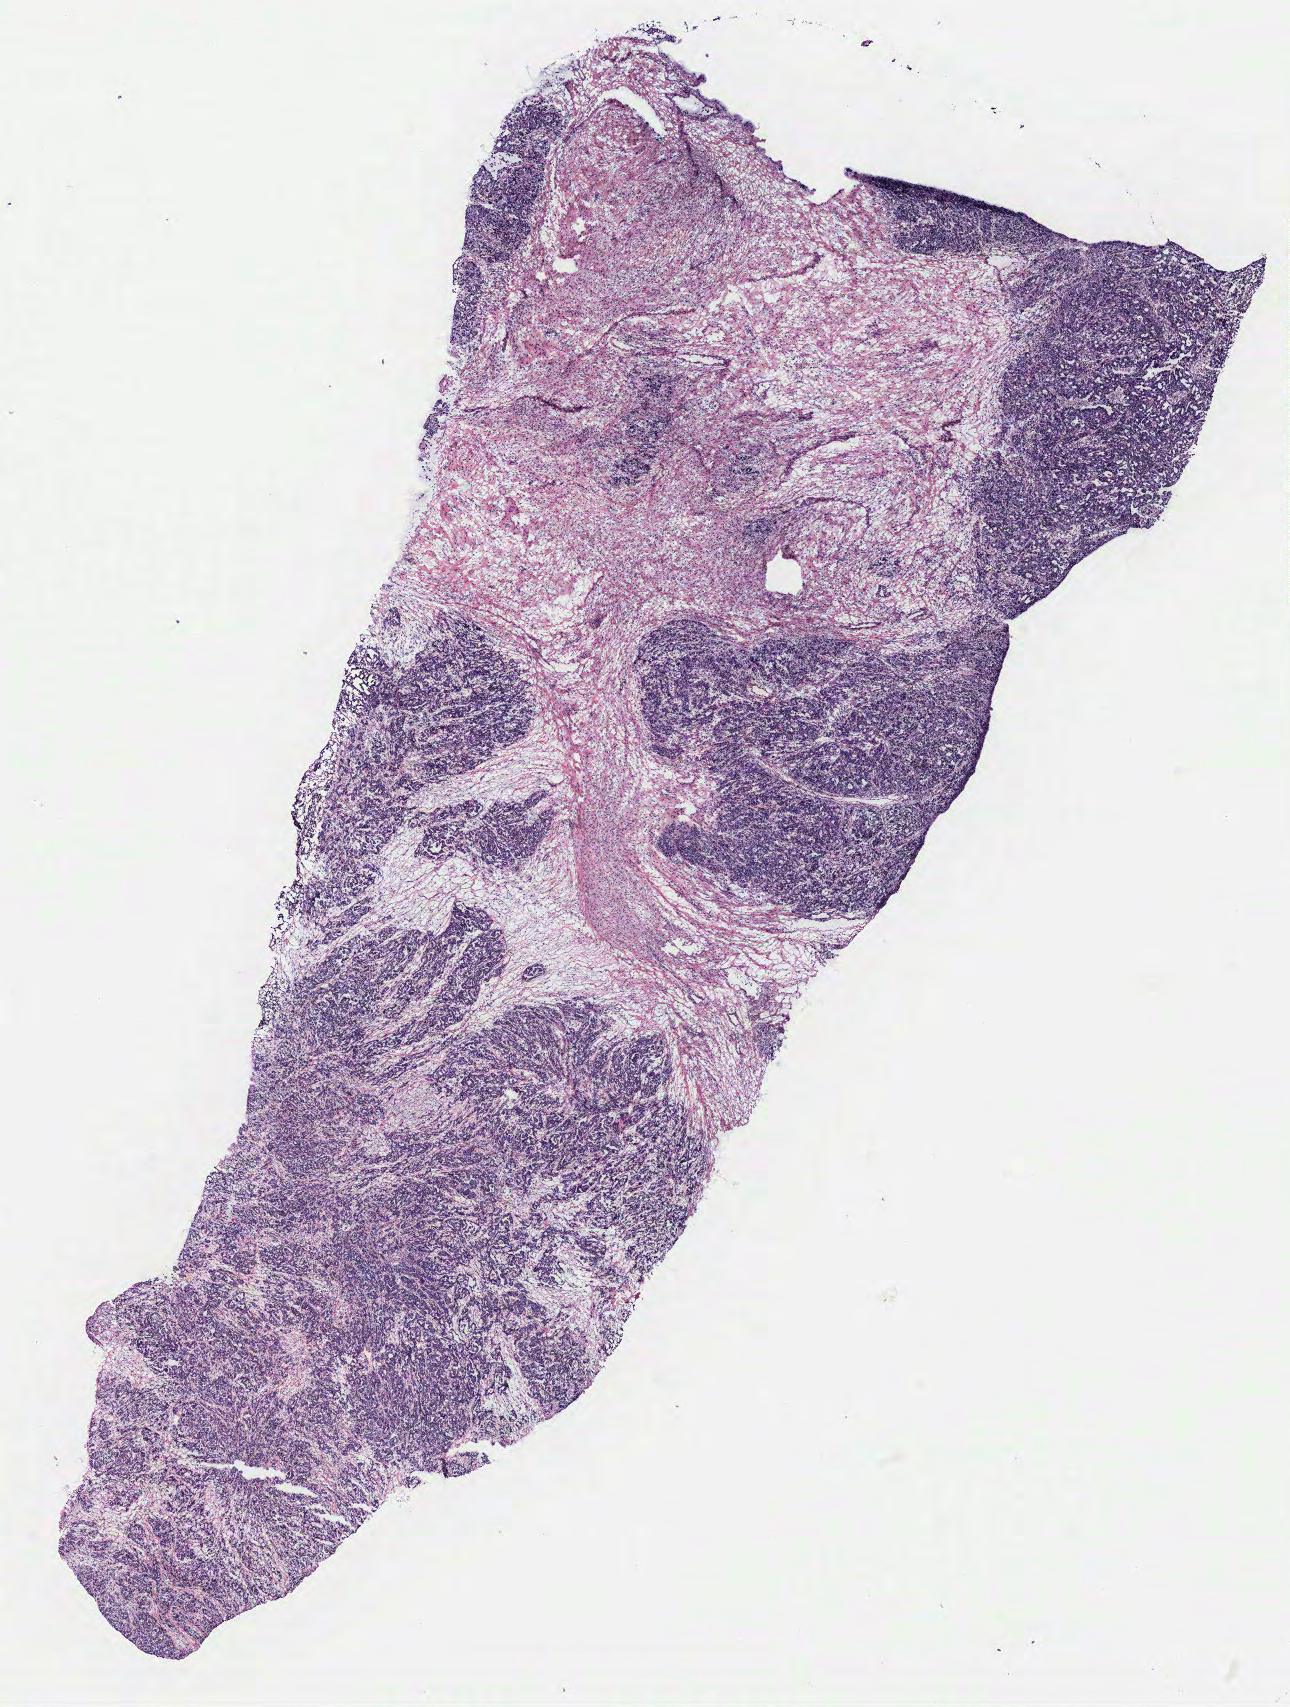
Digitized H&E tissue section (whole slide), whole scanned area (about 10.3 x 13.7 mm) shown as a low-resolution overview. Tumour tissue sample, ovary. 52-year-old female patient.
Diagnosis: Serous adenocarcinoma, NOS (fallopian tube). Primary tumour site (as recorded): fallopian tube.